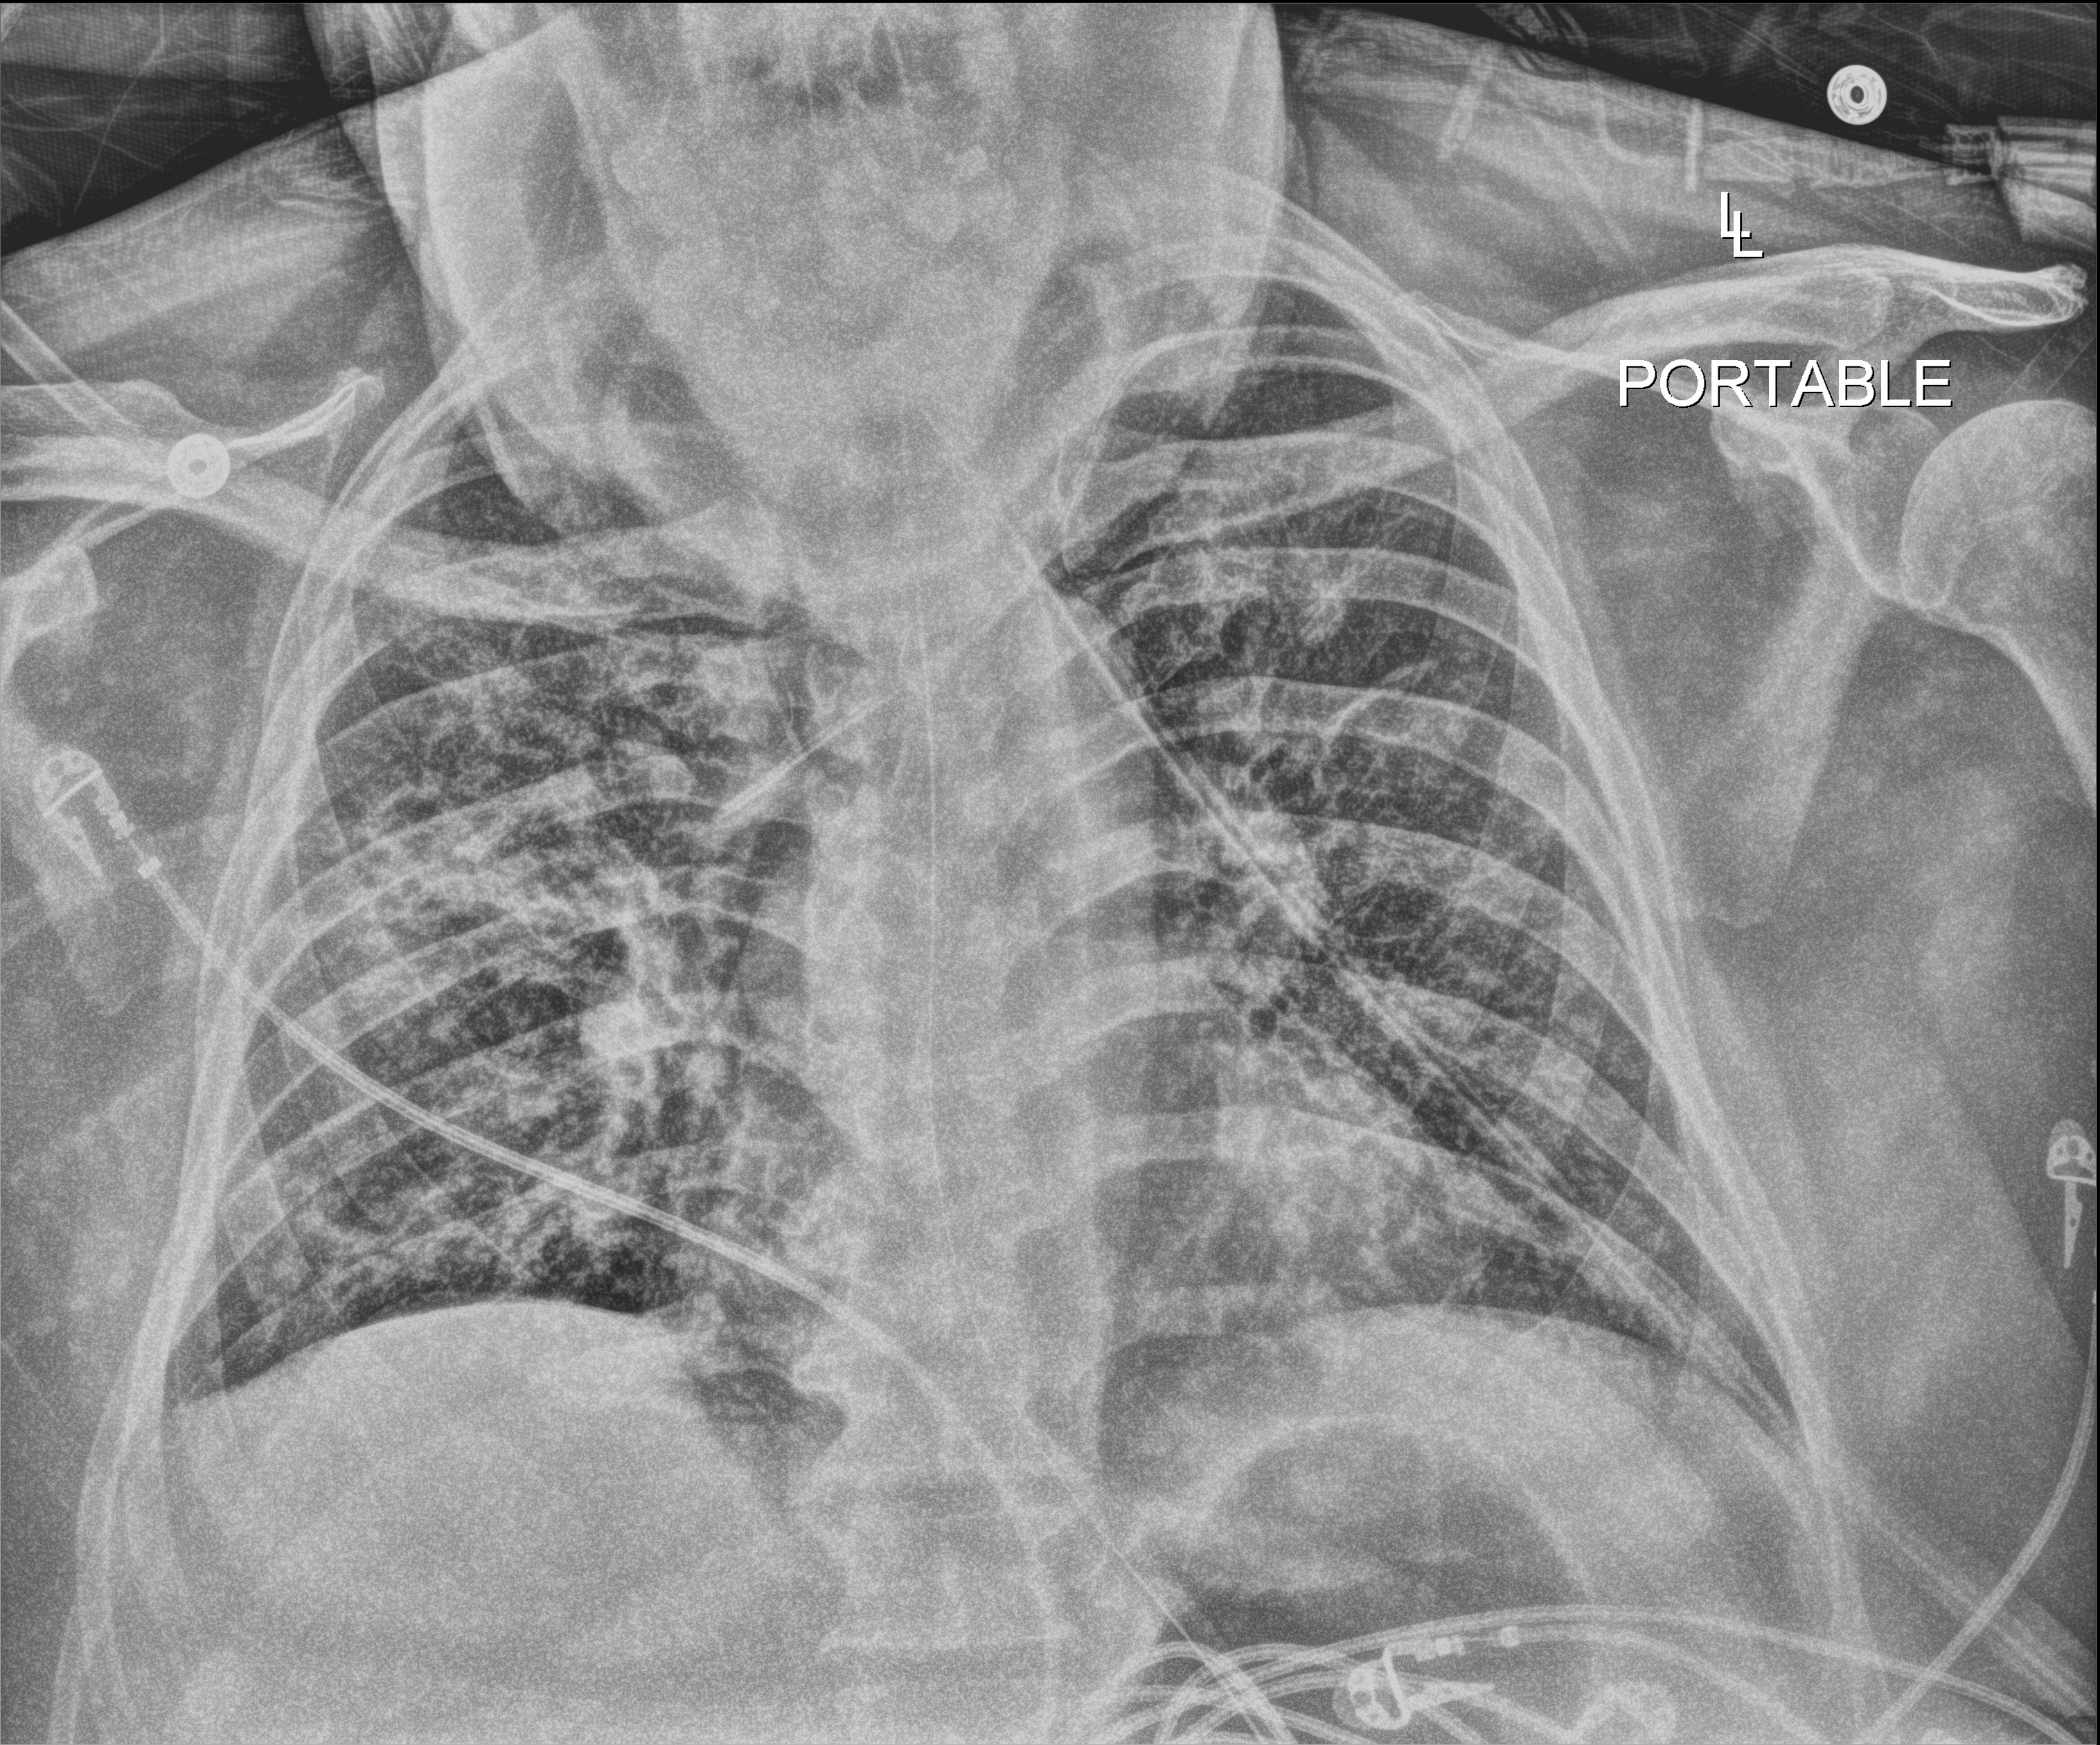
Chest radiograph (digital radiography), anteroposterior (AP) projection. Patient hospitalised with COVID-19; male, aged 18–59 years.
Admission-level facts for this patient (not findings on this image; timing relative to this image not recorded): length of hospital stay: 47 days; admitted to intensive care during this hospital stay: yes; mechanically ventilated during this hospital stay: yes.